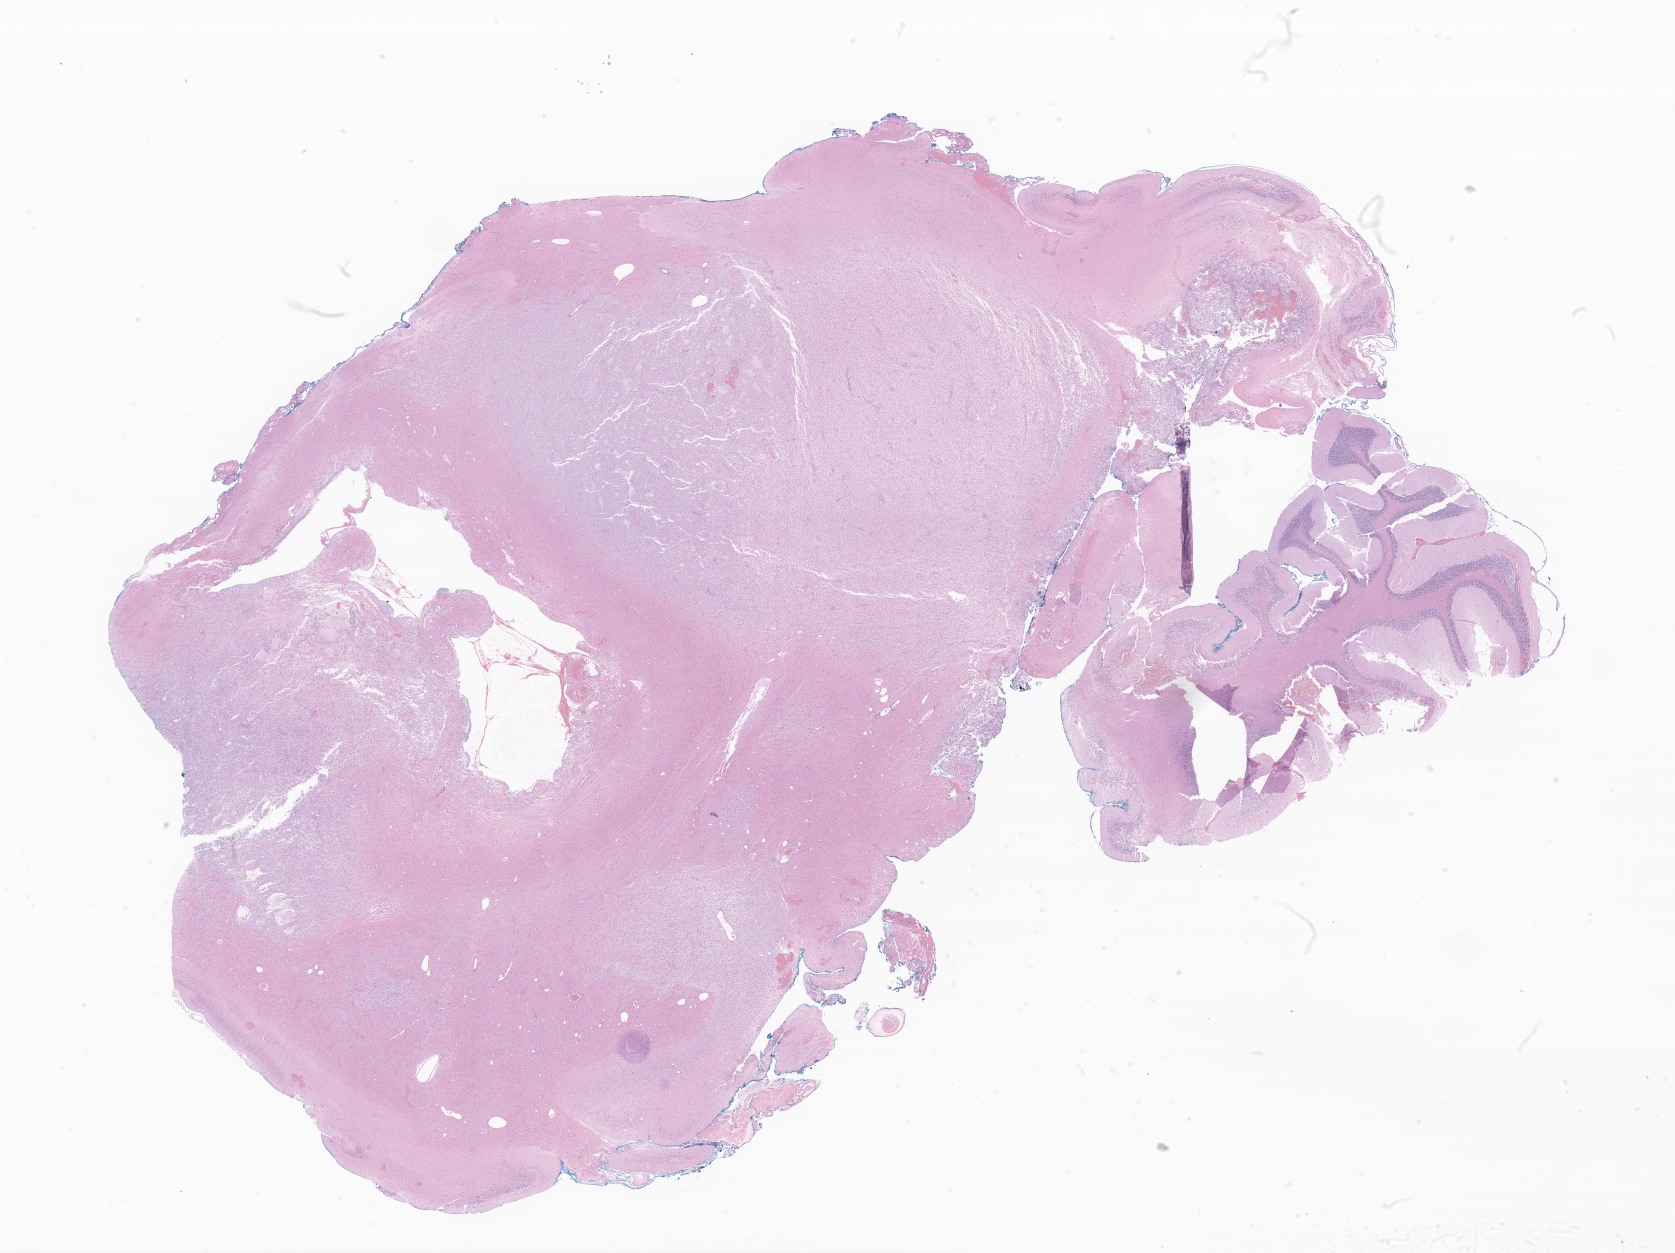
Whole-slide image, hematoxylin and eosin (H&E) stain of tumor tissue from the brain — whole scanned area (about 28.3 x 21.1 mm) shown as a low-resolution overview. Formalin-fixed, paraffin-embedded (FFPE) tissue. Female patient, age 92 months (7 years 8 months).
Diagnosis (ICD-O-3 morphology term): Neoplasm, uncertain whether benign or malignant.